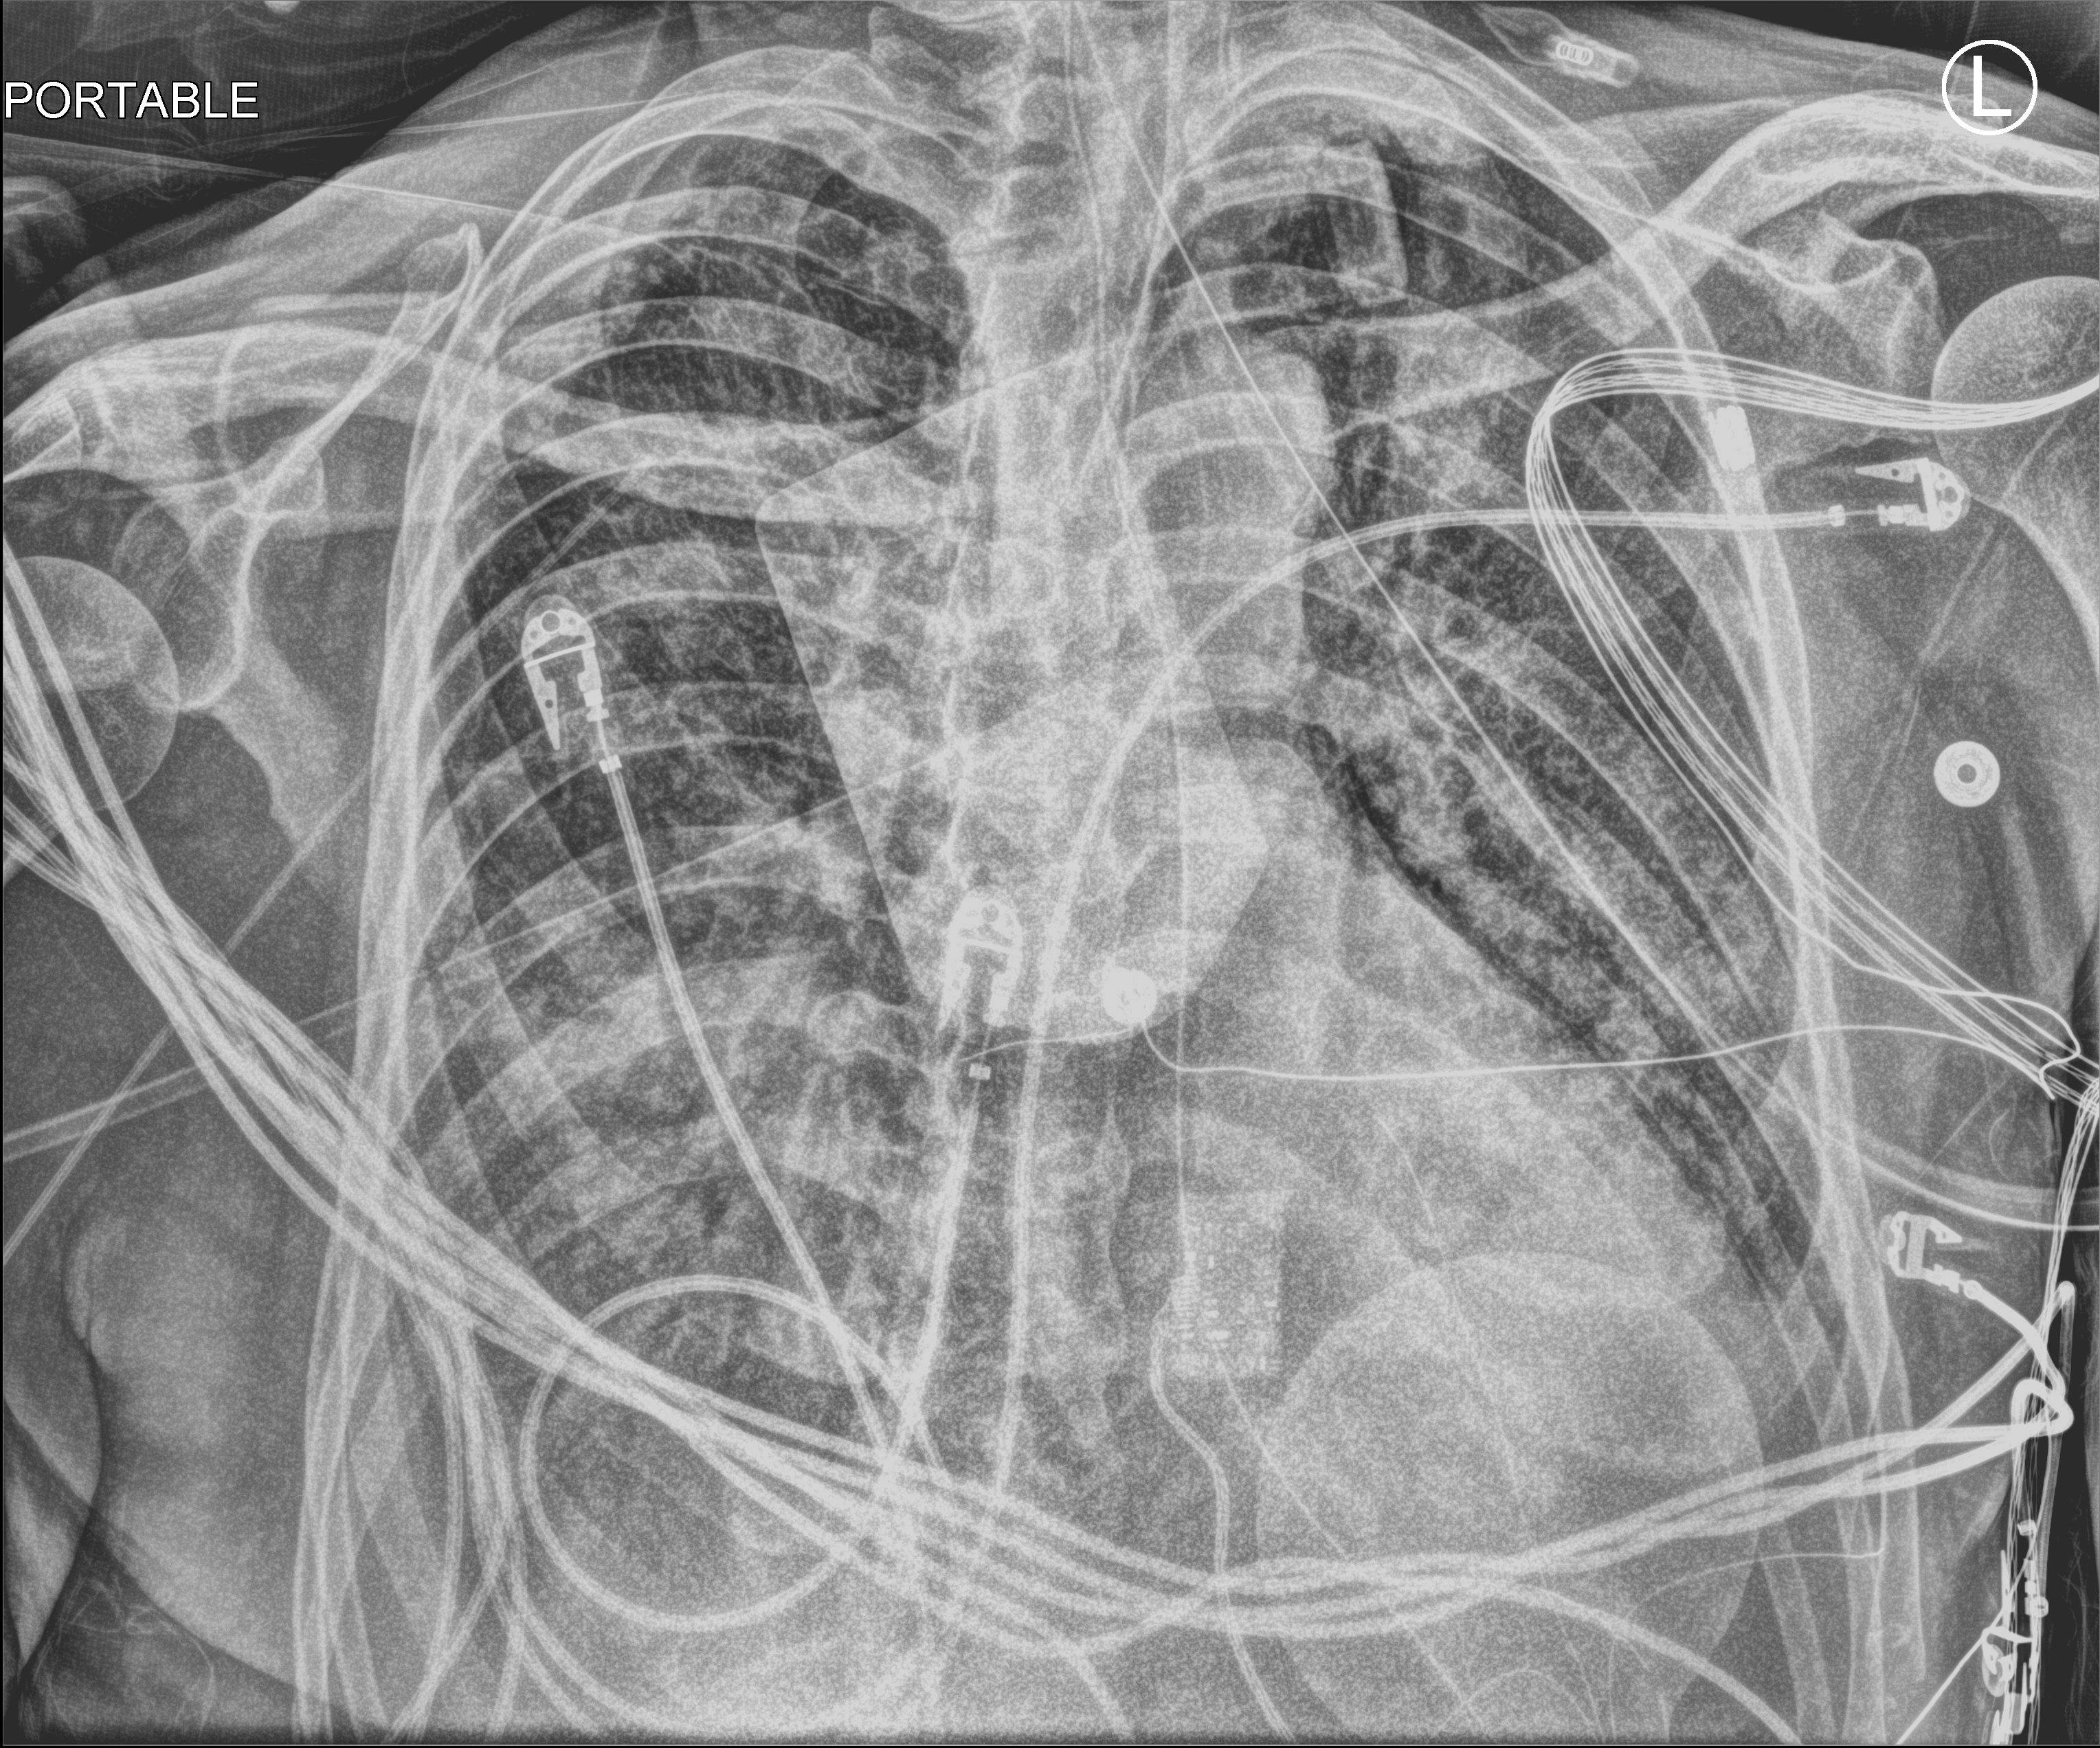
Portable chest radiograph; anteroposterior (AP) projection. Patient hospitalised with COVID-19; male, aged 60–74 years.
Admission-level facts for this patient (not findings on this image; timing relative to this image not recorded): mechanically ventilated during this hospital stay: yes; chronic kidney disease (admission record): no; admitted to intensive care during this hospital stay: yes.